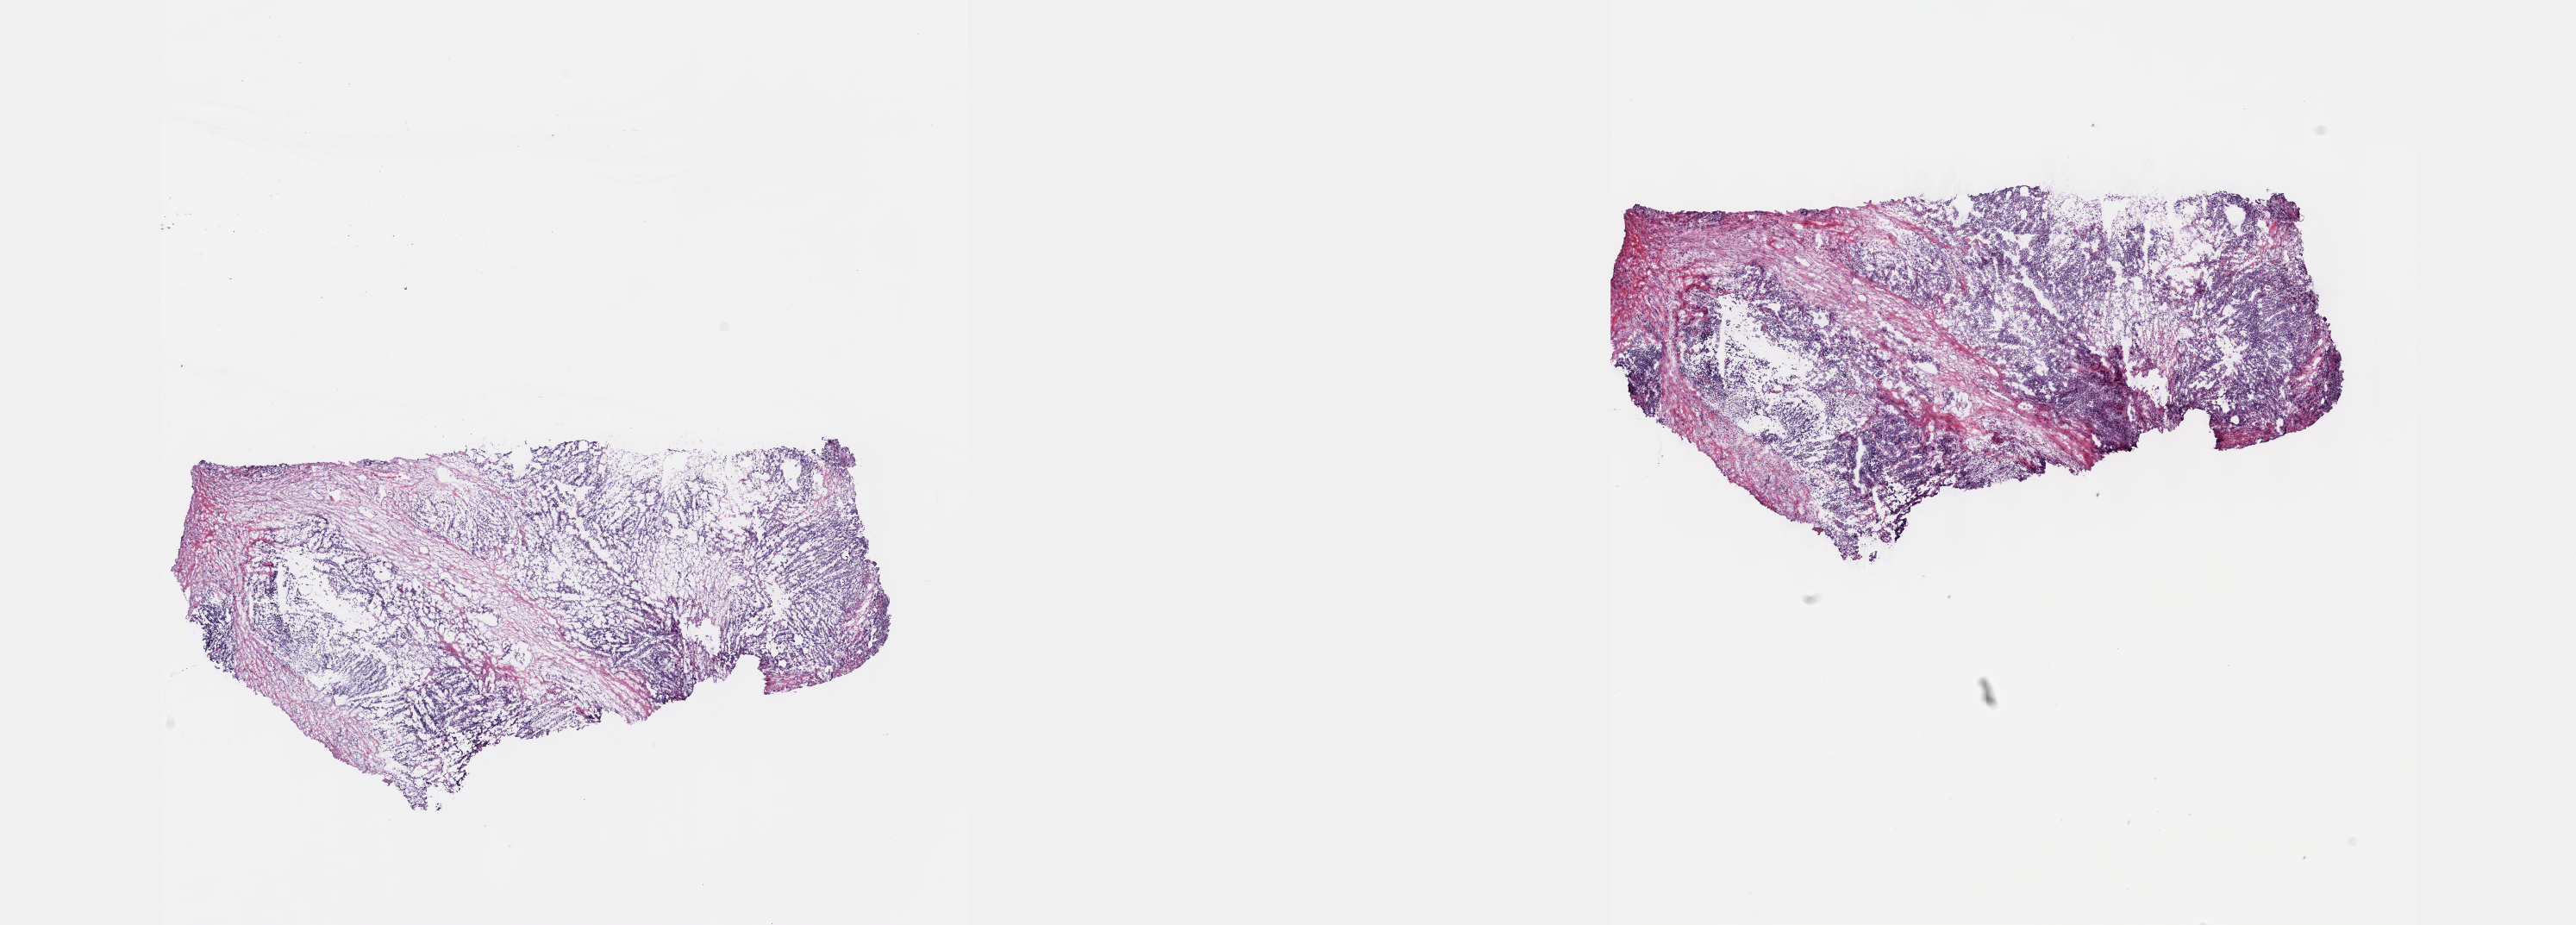
H&E whole-slide image, a low-resolution overview of the entire scanned area, about 24.1 x 8.7 mm, frozen section from the top of the tissue portion, primary tumour sample from the testis. Patient: male, age at initial diagnosis 28 years. Composition of this section per pathologist review: tumour cells 70%, tumour nuclei 90%, normal cells 0%, stromal cells 30%, necrosis 0%. Infiltration values recorded for this section: lymphocyte infiltration 0%, monocyte infiltration 0%, neutrophil infiltration 0%.
* laterality: right
* AJCC pathologic stage: IIIB
* histologic diagnosis: Teratoma, malignant, NOS